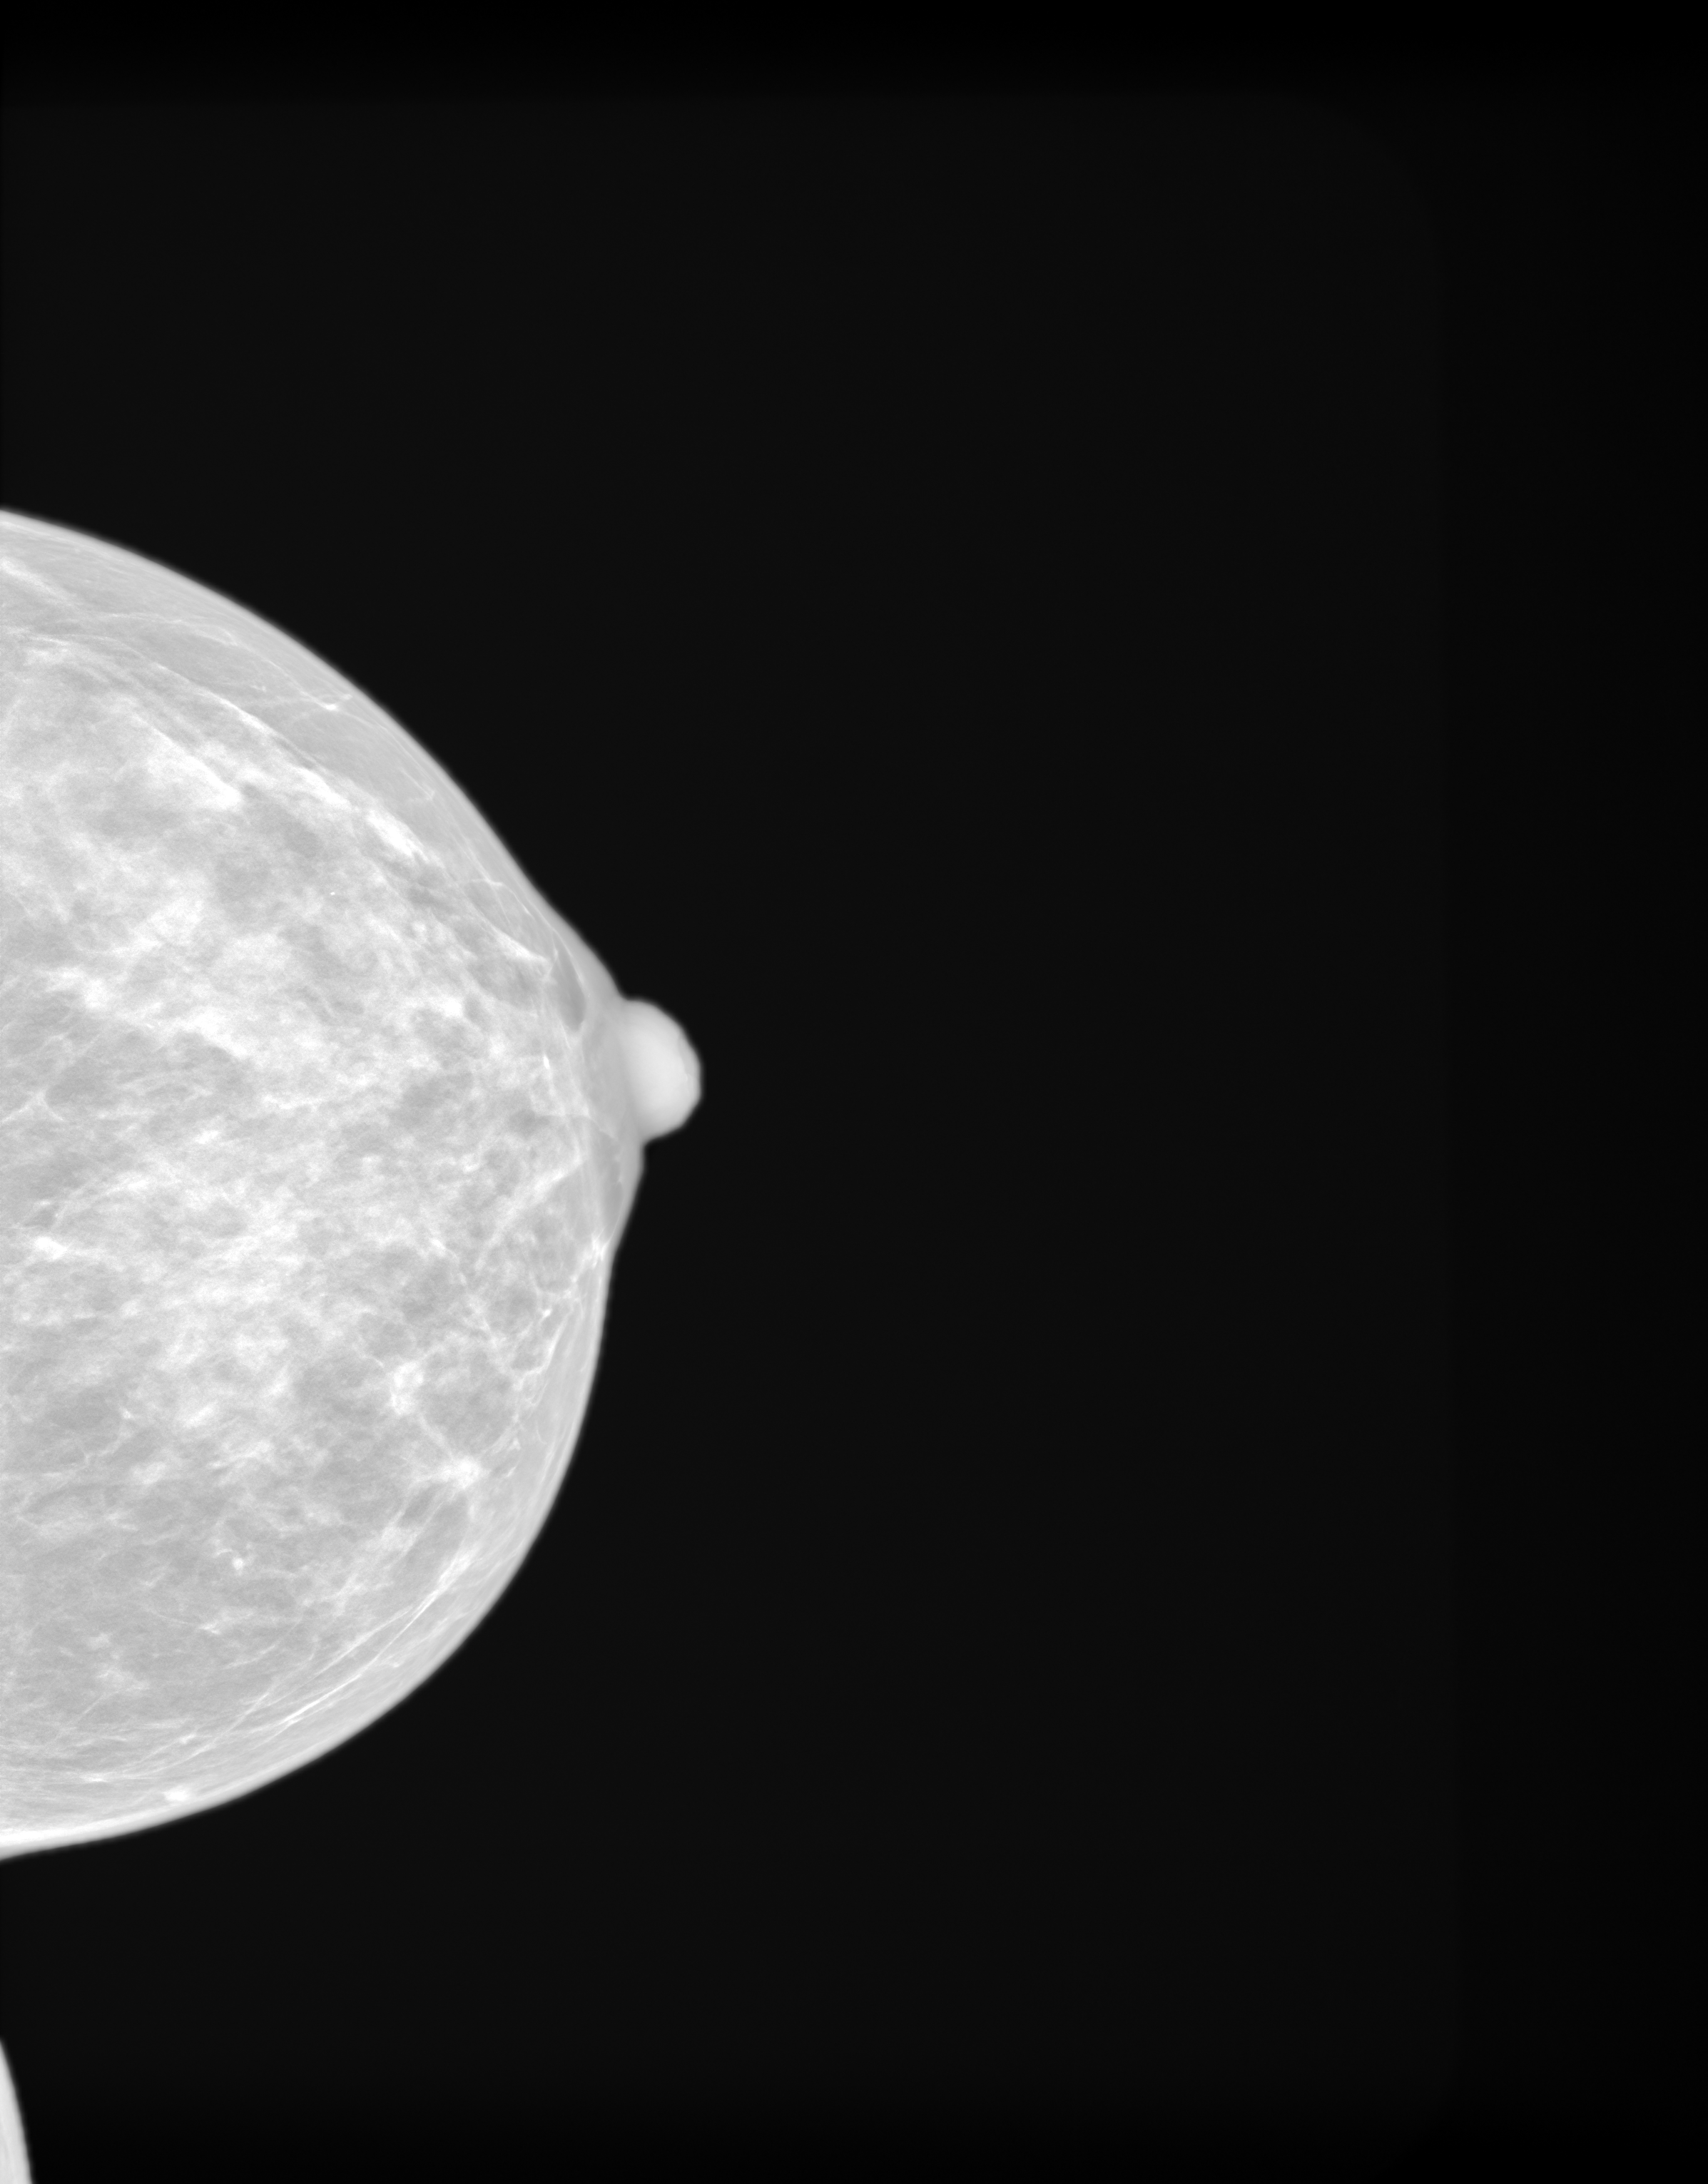
Annual screening mammography examination, system: SenoIris_1SP2(440). Female patient, age 43 years.
Image type: synthesized 2-D view from tomosynthesis. Breast: left. Projection: CC view.